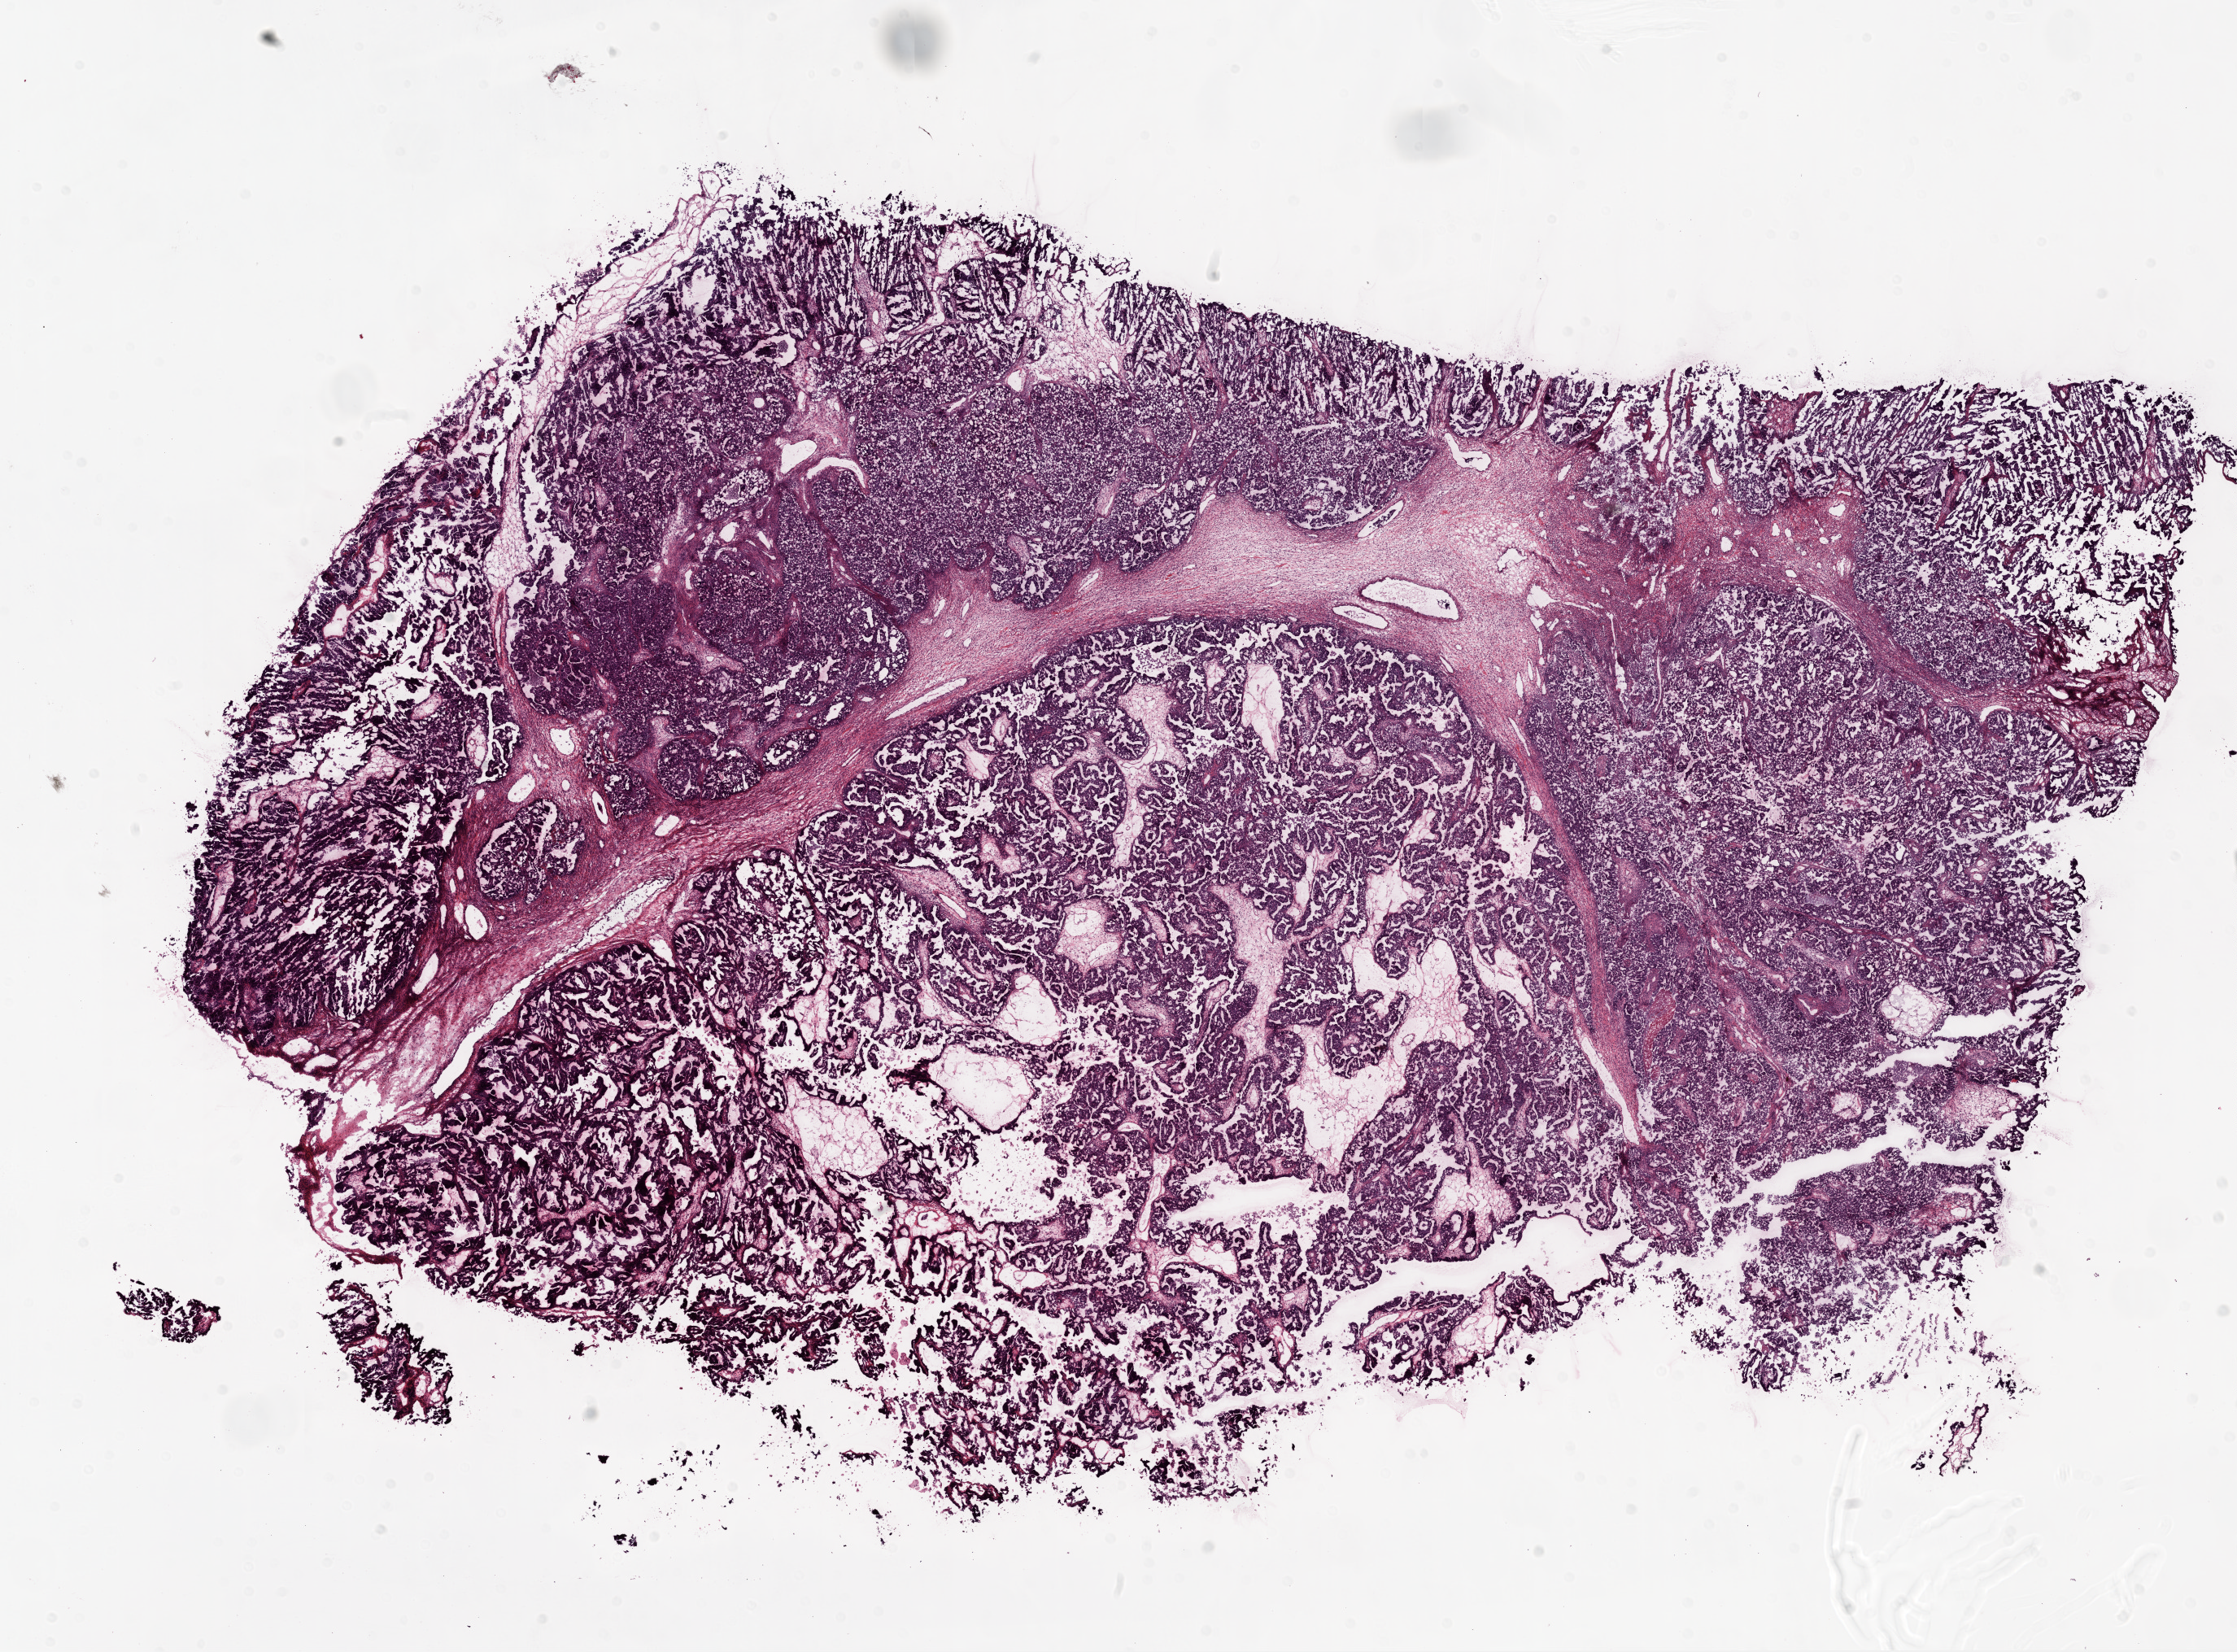
Whole-slide histology image, Hematoxylin and eosin (H&E) stained — whole scanned area (about 22.1 x 16.3 mm, slide scanned at 20x) shown as a low-resolution overview; frozen section from the top of the tissue portion; ovary, primary tumour sample. Patient: female, age at initial diagnosis 50 years. Histologic grade: G3 (poorly differentiated). Composition of this section per pathologist review: tumour cells 90%, tumour nuclei 80%, normal cells 0%, stromal cells 10%, necrosis 0%. Infiltration values recorded for this section: lymphocyte infiltration 5%, monocyte infiltration 2%, neutrophil infiltration 0%.
* FIGO stage: IIIC
* histologic diagnosis: Serous cystadenocarcinoma, NOS